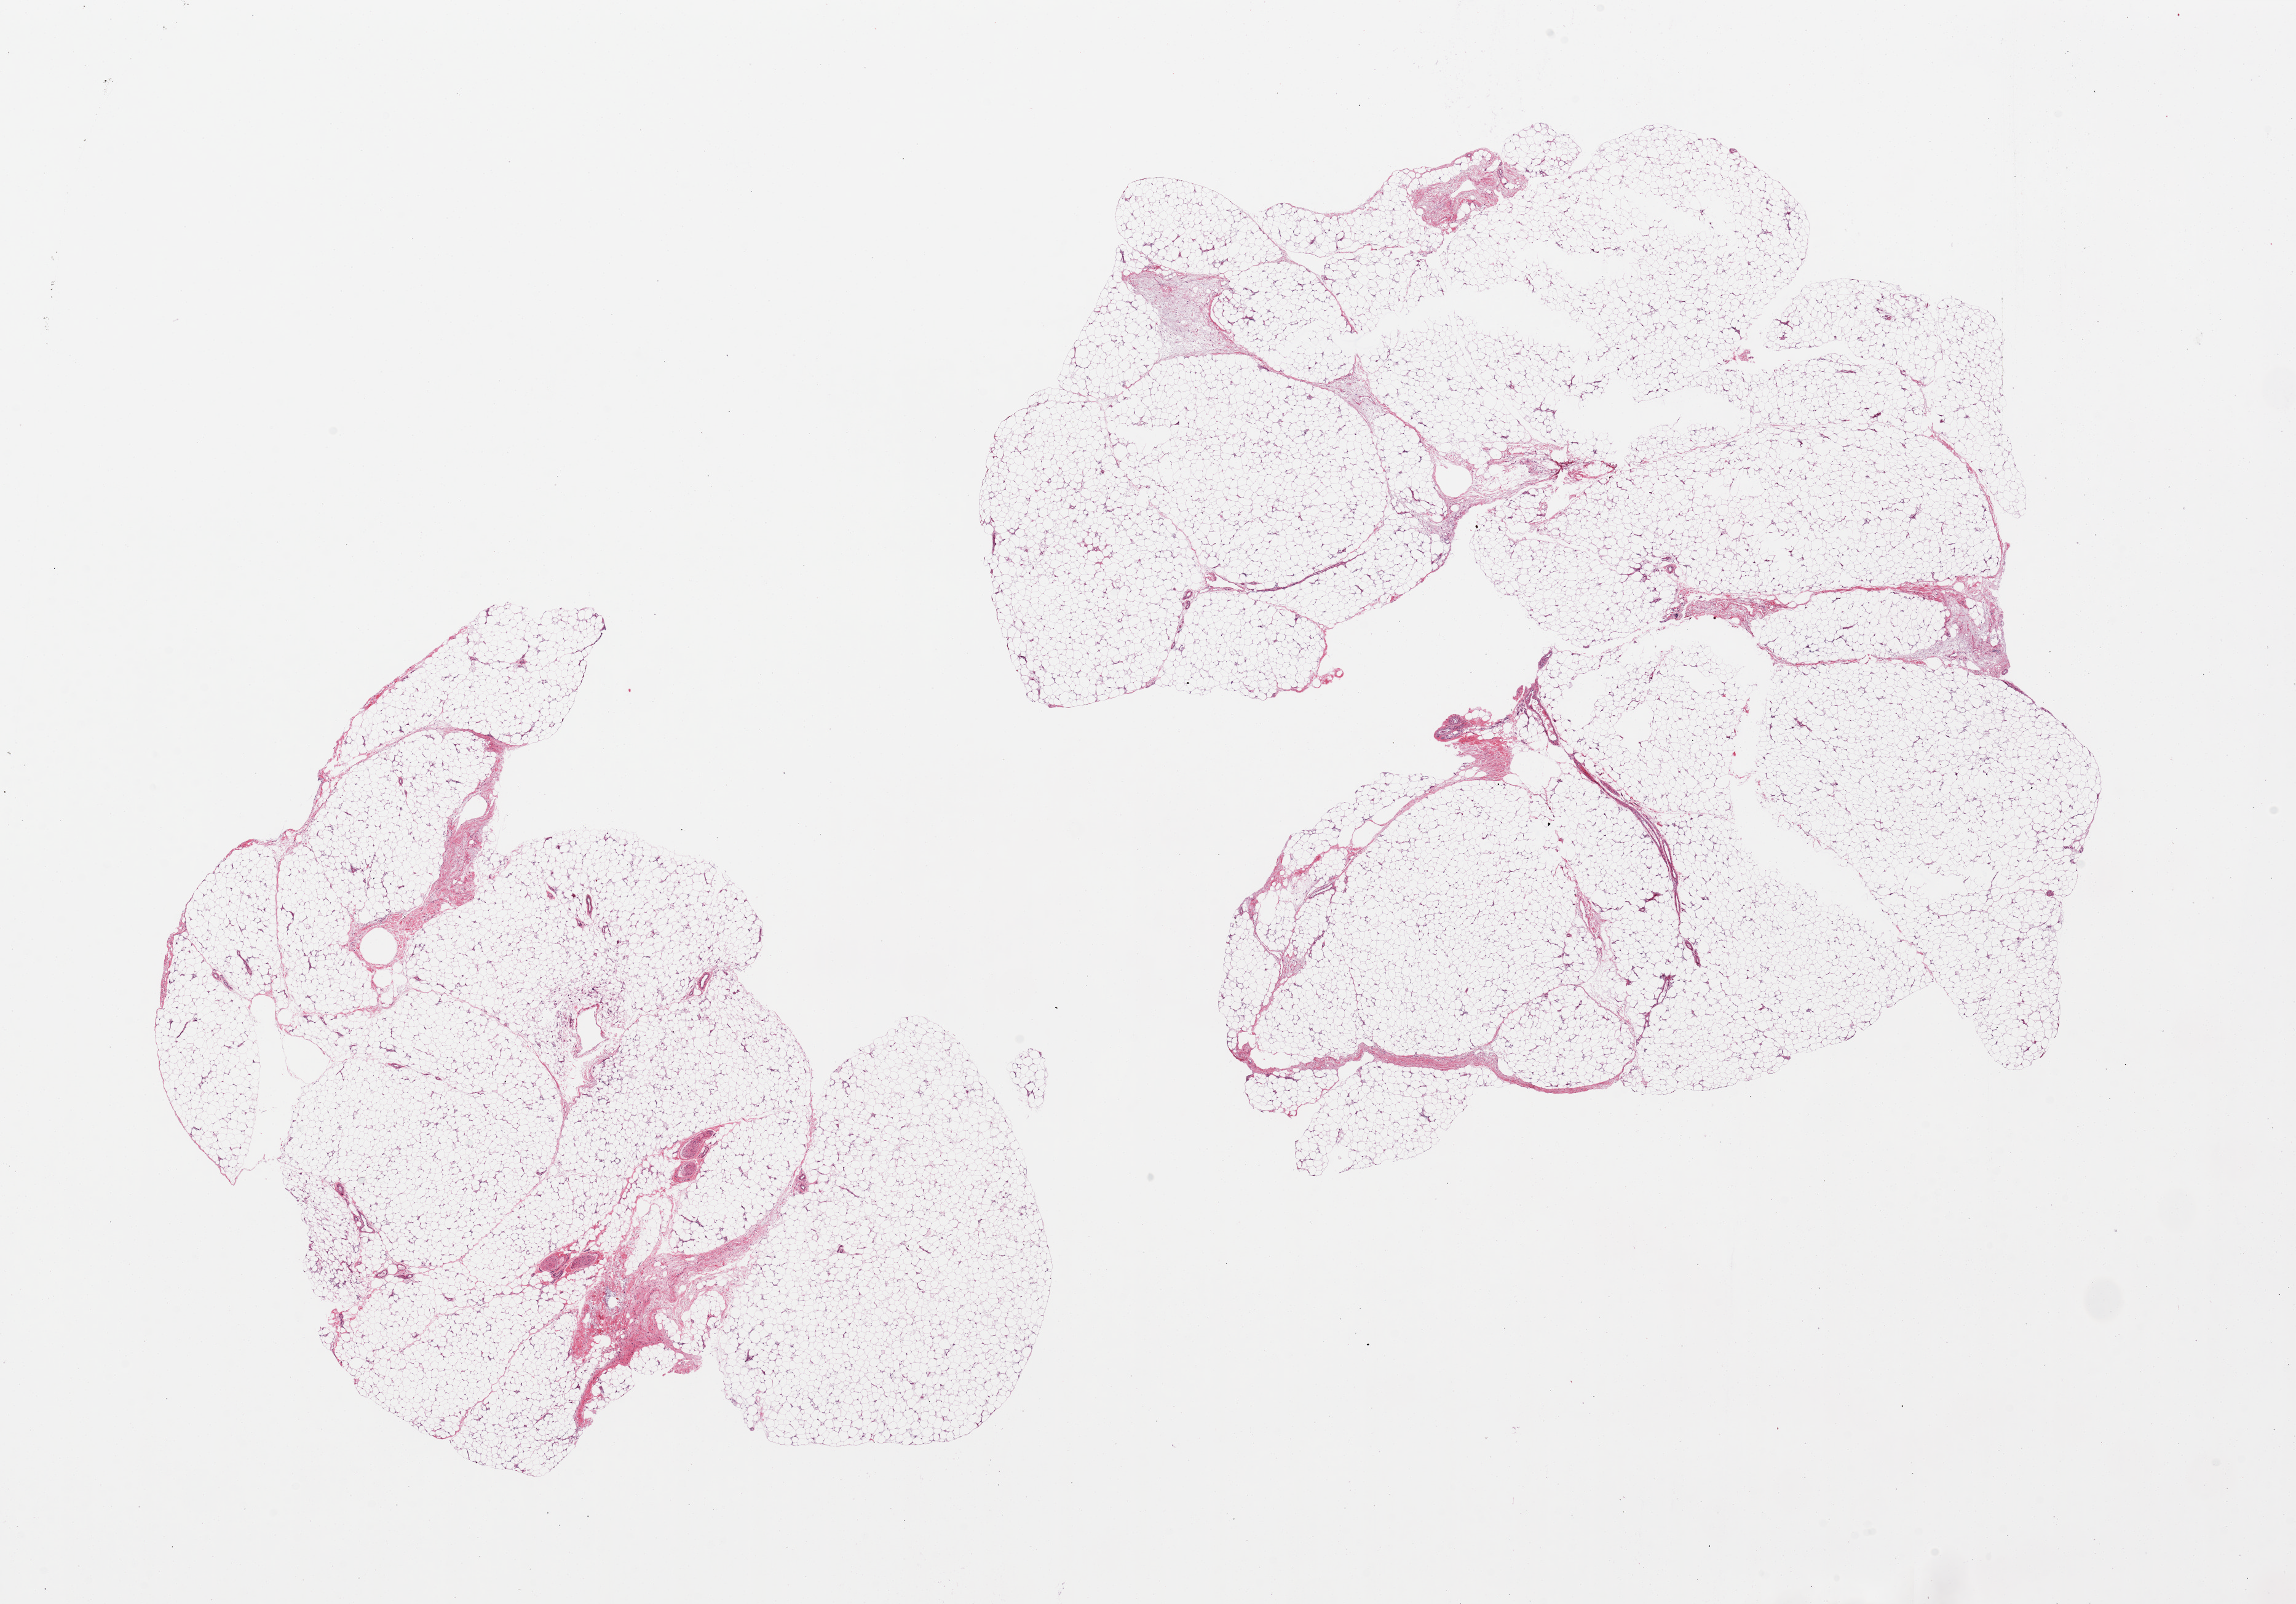
Whole-slide image, haematoxylin and eosin stain, a low-resolution overview of the entire scanned area, about 29.5 x 20.6 mm; PAXgene-fixed, paraffin-embedded tissue; target tissue: adipose tissue; tissue donor sample. Donor: male.
Pathologist's review note for this sample: 2 pieces.